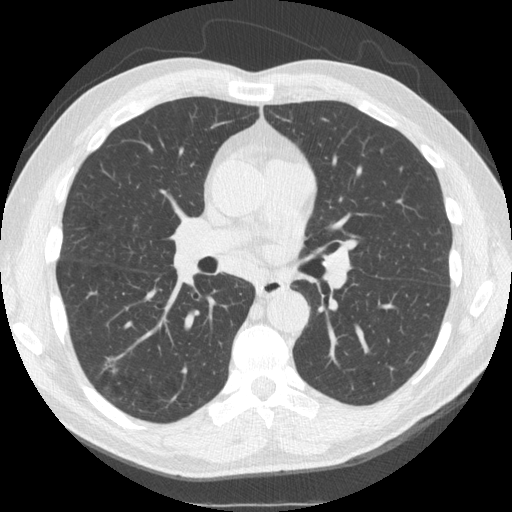
Low-dose screening chest CT, one axial slice. Position 89 of 162 along the scan axis. Reconstruction kernel STANDARD. Lung window (W 1500 / L -600 HU). 2.5 mm slice thickness. 512 × 512 image matrix, field of view 360 × 360 mm.
Outlined on this slice (expert manual segmentation):
- lesion 1 (nodule, lower lobe of right lung): bounding box <103,356,119,373> (left, top, right, bottom; pixels)